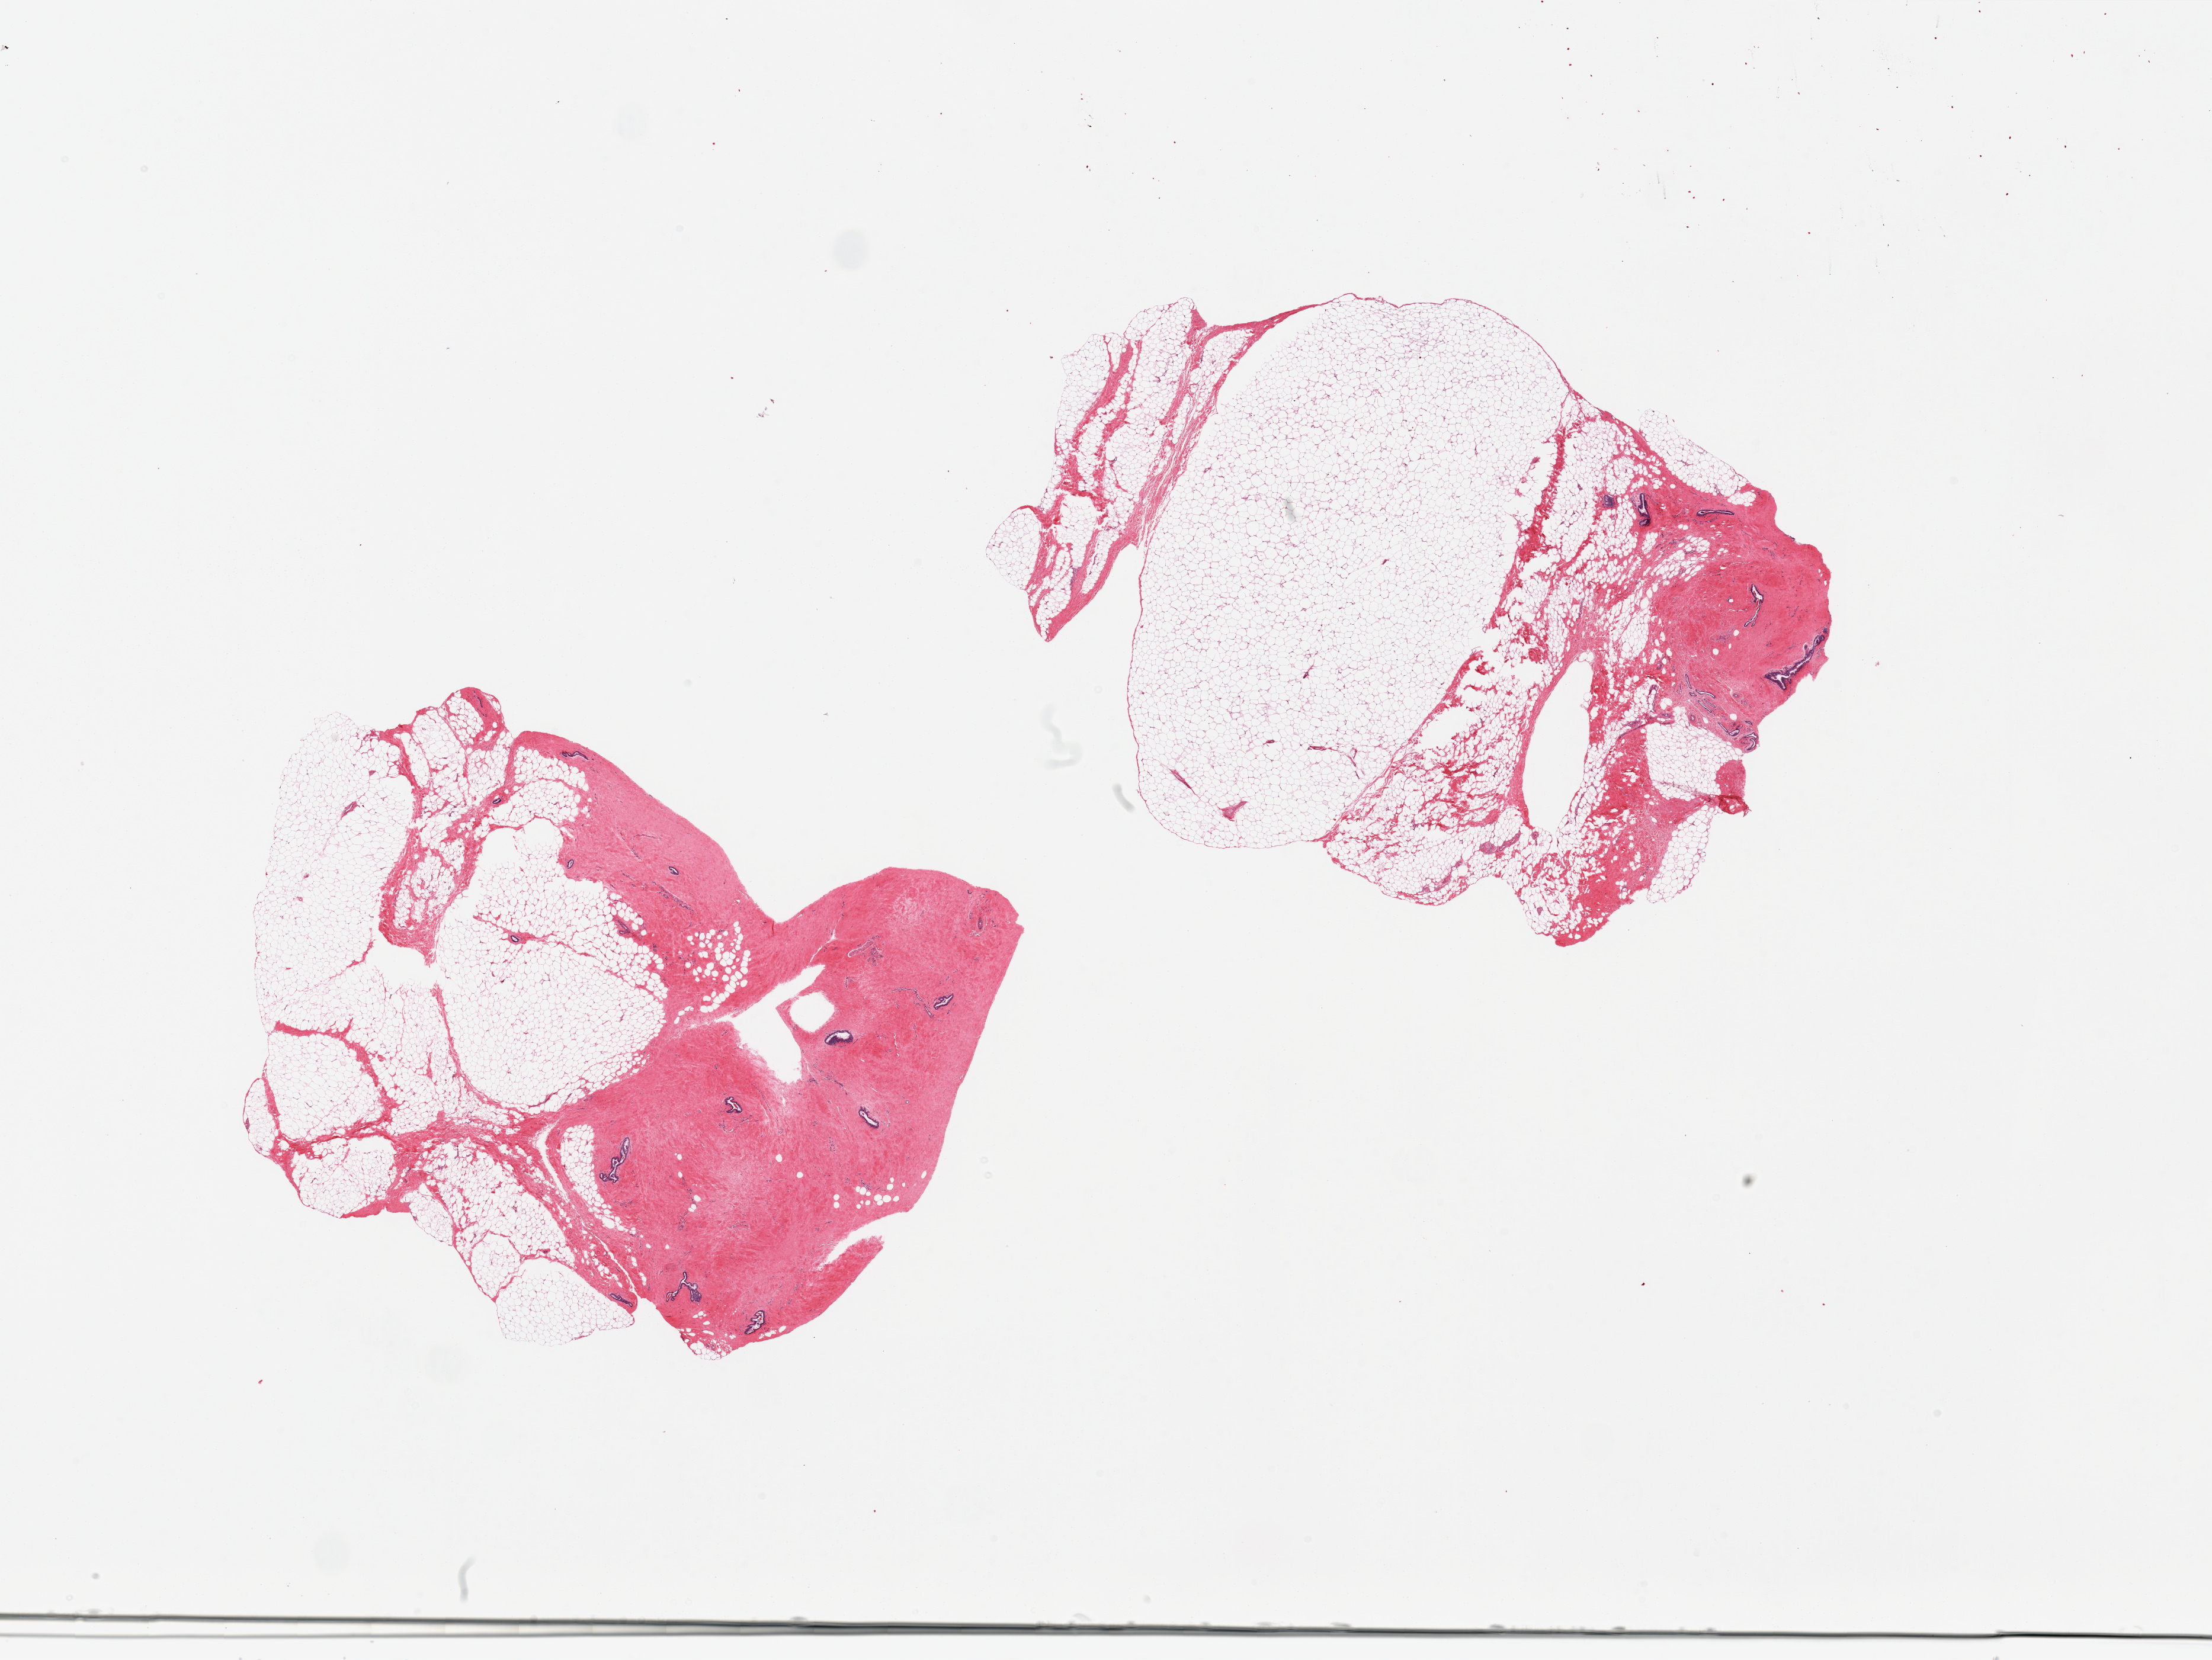
Digitized hematoxylin and eosin (H&E)-stained section, low-resolution overview of the scanned area, about 29.5 x 22.2 mm (slide scanned at 20x); PAXgene-fixed paraffin-embedded (PFPE) section; section of breast (target tissue); tissue donor sample.
Review note (as recorded): 2 pieces; gynecomastoid hyperplasia; 1 piece 80% fat, other 50% fat.